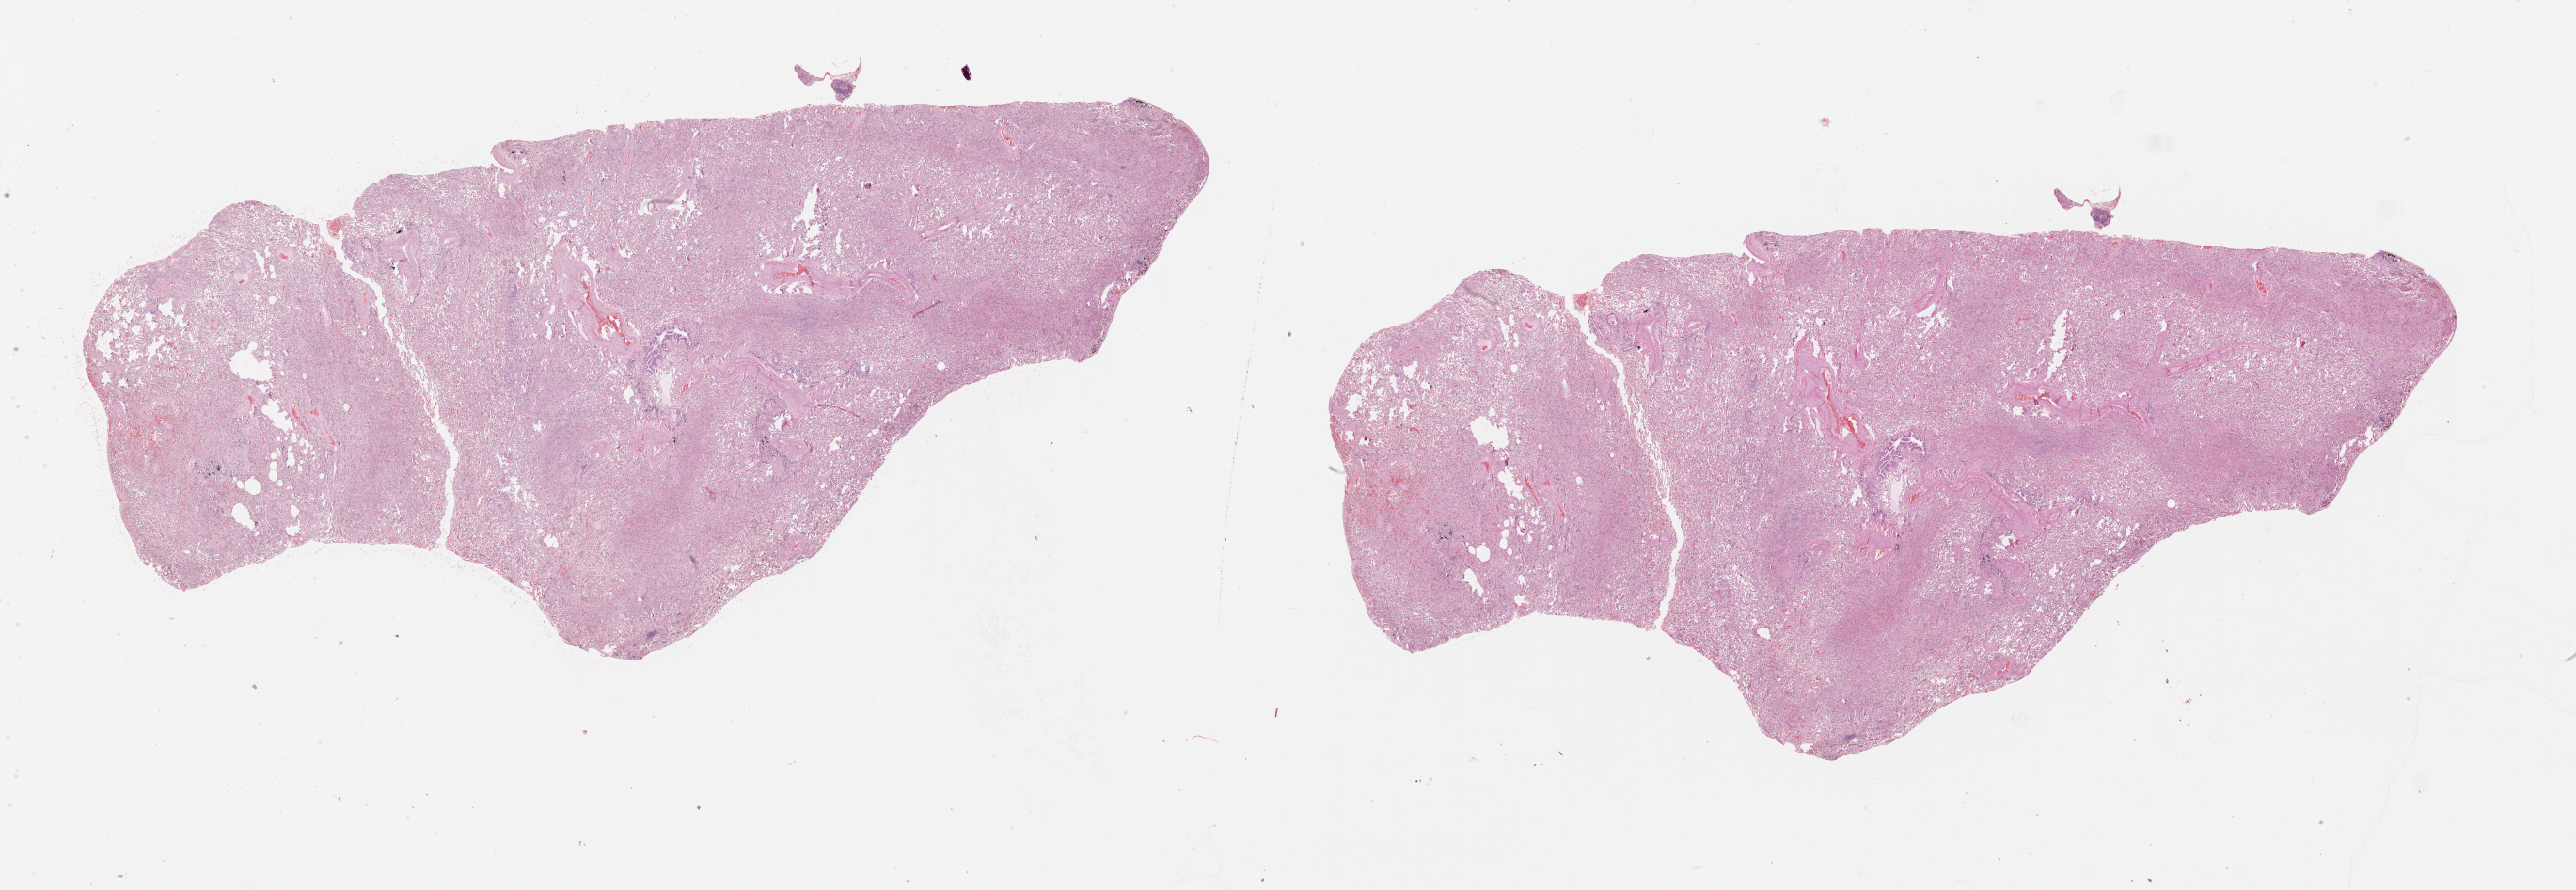
Whole-slide histology image, Hematoxylin and eosin (H&E) stained — a low-resolution overview of the entire scanned area, about 44.1 x 15.2 mm. Normal (non-tumour) tissue sample, lung. Male, 56 y/o.
This section: normal (non-tumour) tissue from the same patient. Patient diagnosis (cohort enrolment): squamous cell carcinoma (lung).